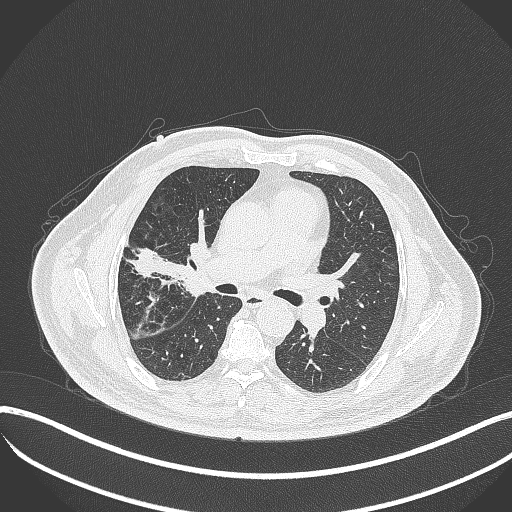
Chest CT, one axial slice; slice 208 of 401 in the series (ordered by position); 120 kVp; lung window (W 1500 / L -600 HU); 1 mm slice thickness; 512 × 512 image matrix, field of view 400 × 400 mm. Male patient, age 72 years. From the clinical record (not read from this slice): clinical TNM (as recorded): T1c N0 M0; histopathological grade: G2.
Outlined on this slice (rectangle marked by the reading radiologist):
- lung tumour (recorded histology: squamous cell carcinoma): bounding box [x1, y1, x2, y2] px = [169, 241, 219, 307]